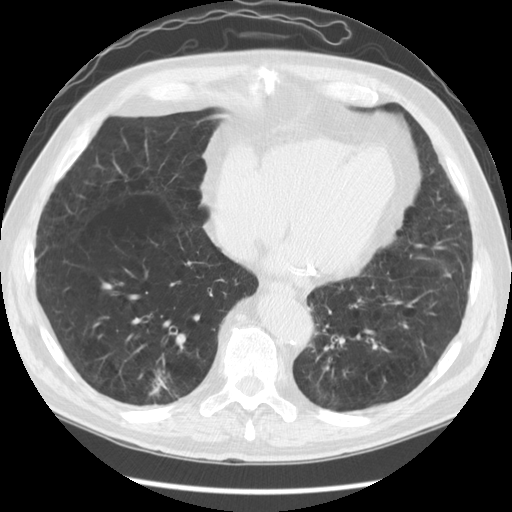
Low-dose screening chest CT, one axial slice. Slice 47 of 141 in the series (ordered by position). Lung window (W 1500 / L -600 HU). 512 × 512 image matrix, field of view 370 × 370 mm.
Annotated regions visible in this slice (outlined manually by an expert reader):
- lesion 1 (tumor, lower lobe of right lung): bounding box (x1, y1, x2, y2) in pixels: (149, 370, 169, 396)